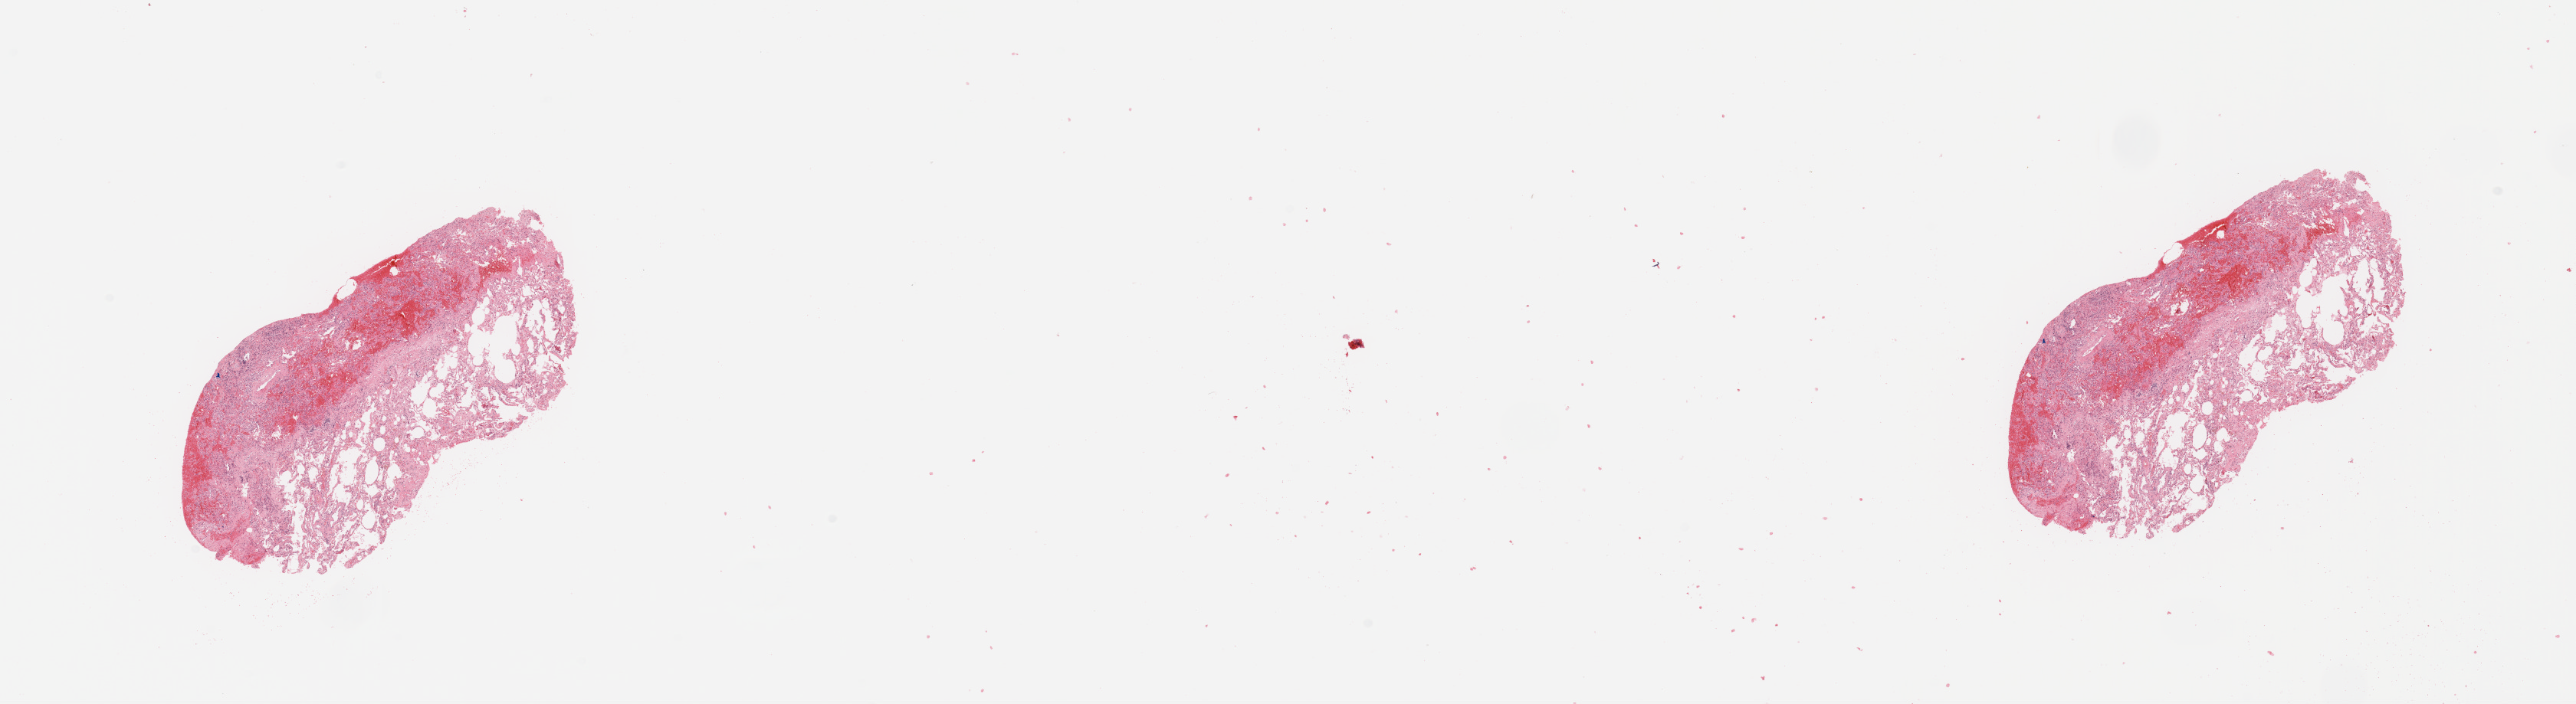
H&E whole-slide image, low-resolution overview of the scanned area, about 26.6 x 7.3 mm (slide scanned at 20x). Normal (non-tumour) tissue sample, sampled site: lung. 71-year-old male patient.
- this section: normal (non-tumour) tissue from the same patient
- patient diagnosis: Adenocarcinoma, NOS